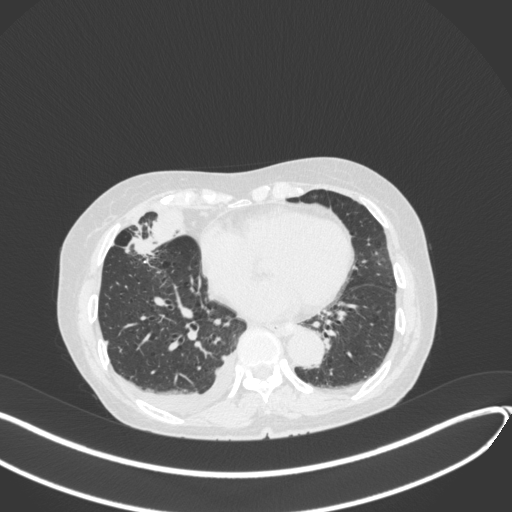
Chest CT, one axial slice; slice 142 of 418 in the series (ordered by position); reconstruction kernel B31f; 120 kVp; lung window (W 1500 / L -600 HU); 1 mm slice thickness; 512 × 512 image matrix, field of view 400 × 400 mm. Female patient, age 75 years. Case-level facts recorded for this patient, not image findings: clinical TNM (as recorded): T2a N3 M0.
Annotated regions visible in this slice (rectangle marked by the reading radiologist):
- lung tumour (recorded histology: adenocarcinoma): bounding box <124,232,159,259> (left, top, right, bottom; pixels)